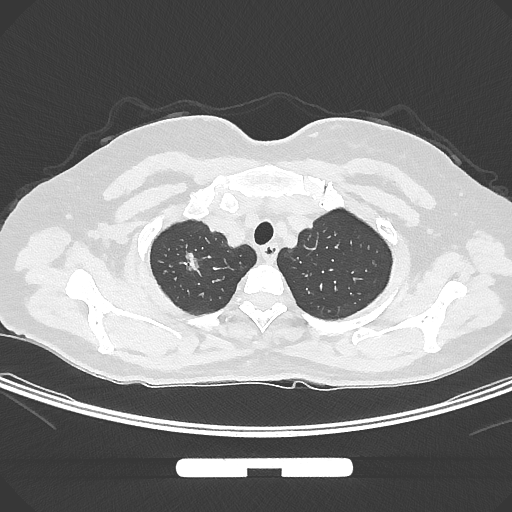
Chest CT, one axial slice. Position 258 of 294 along the scan axis. 120 kVp. Lung window (W 1500 / L -600 HU). 1 mm slice thickness. 512 × 512 image matrix, field of view 369 × 369 mm. Patient: female, 58 years. From the clinical record (not read from this slice): clinical TNM (as recorded): T1b N0 M0; histopathological grade: G2-3.
Outlined on this slice (bounding box drawn by a radiologist):
- lung tumour (recorded histology: adenocarcinoma): box from (x=177, y=243) to (x=207, y=286) px